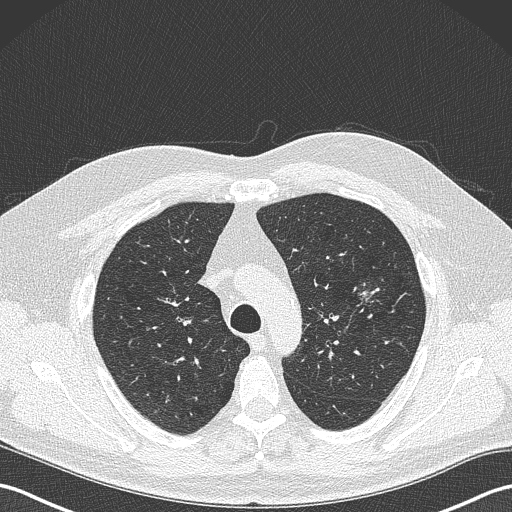
Low-dose screening chest CT, axial slice, baseline screening round, lung window (W 1500 / L -600 HU), 1 mm slice thickness, 120 kVp, 512 × 512 image matrix, field of view 350 × 350 mm. Male participant, aged 61 years at enrolment. Former smoker at enrolment.
Expert reader's lesion annotation, bounding box <350,282,385,312> (left, top, right, bottom; pixels). The screening reader recorded 2 non-calcified nodules or masses ≥4 mm on this exam (left upper lobe, lingula); which of them this box marks is not recorded.